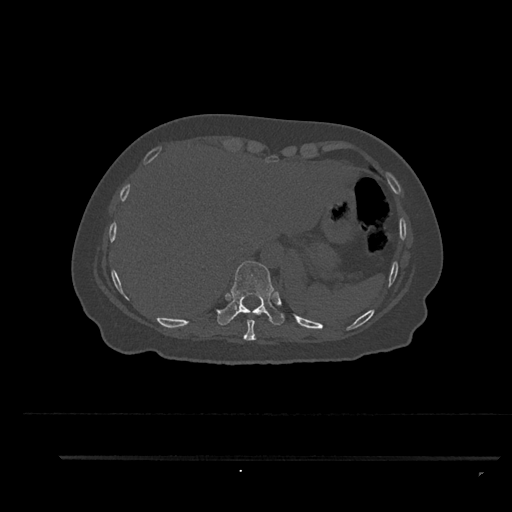
CT including the spine, one axial slice; bone window (W 1800 / L 400 HU); 512 × 512 image matrix, field of view 408 × 408 mm. Patient: female, 44 years. Case-level facts recorded for this patient, not image findings: primary cancer: renal.
Outlined on this slice (semi-automatic segmentation, software-assisted and operator-edited):
- T10 vertebra: box from (x=216, y=261) to (x=285, y=326) px
- T9 vertebra: (x=243, y=320)–(x=256, y=341)